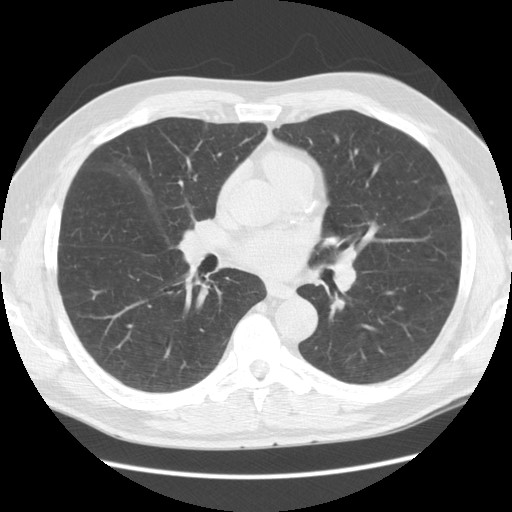
Low-dose screening chest CT, axial slice; second screening round (one year after baseline); lung window (W 1500 / L -600 HU). Male participant, aged 60 years at enrolment. Current smoker at enrolment.
Expert-annotated lung lesion, box from (x=387, y=295) to (x=416, y=323) px. The screening reader recorded 4 non-calcified nodules or masses ≥4 mm on this exam (right lower lobe, right middle lobe, left lower lobe, left upper lobe); which of them this box marks is not recorded. Official screen result: positive, no significant change: stable abnormalities potentially related to lung cancer, unchanged since the prior screening exam. Participant outcome: lung cancer diagnosed 594 days after this screen — large cell neuroendocrine carcinoma, left lower lobe, poorly differentiated (G3), stage IB (AJCC 6th edition), 33 mm at pathology.